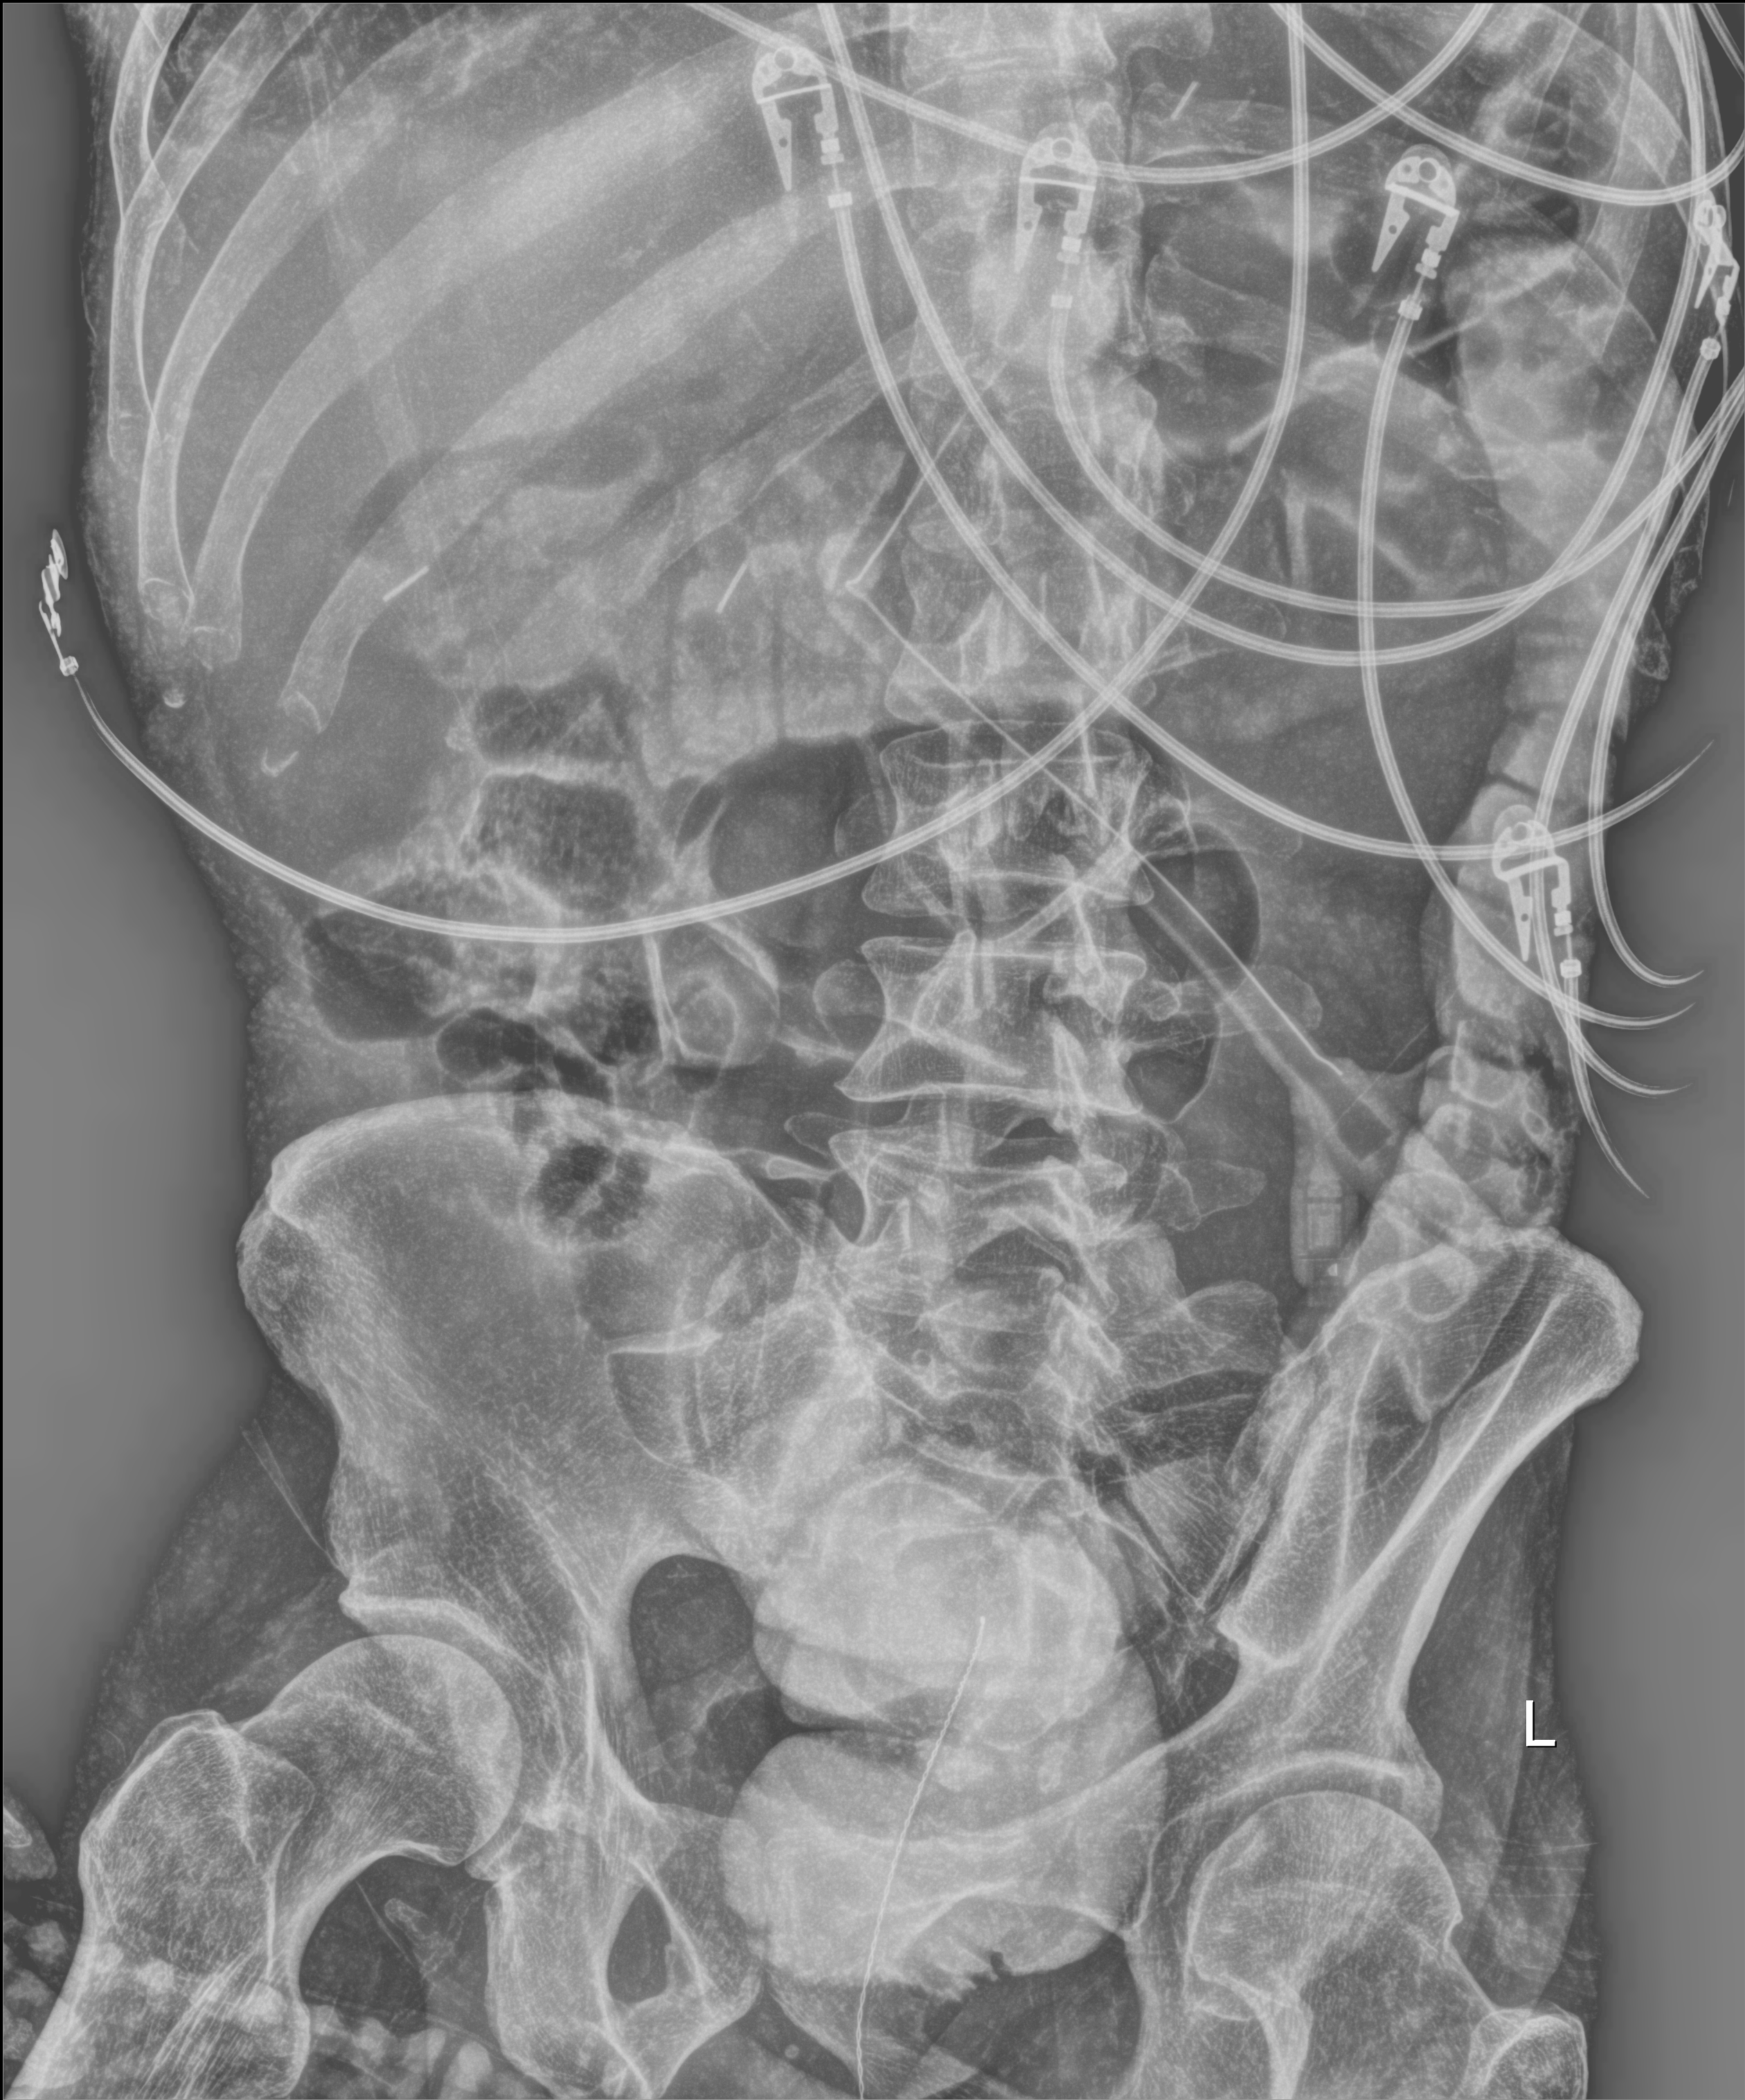
Abdomen X-ray (portable). Male patient hospitalised with COVID-19, age 18–59 years.
Hospital-stay facts (about this admission, not read from this image; timing relative to this image not recorded):
- chronic kidney disease (admission record): no
- mechanically ventilated during this hospital stay: yes
- admitted to intensive care during this hospital stay: yes